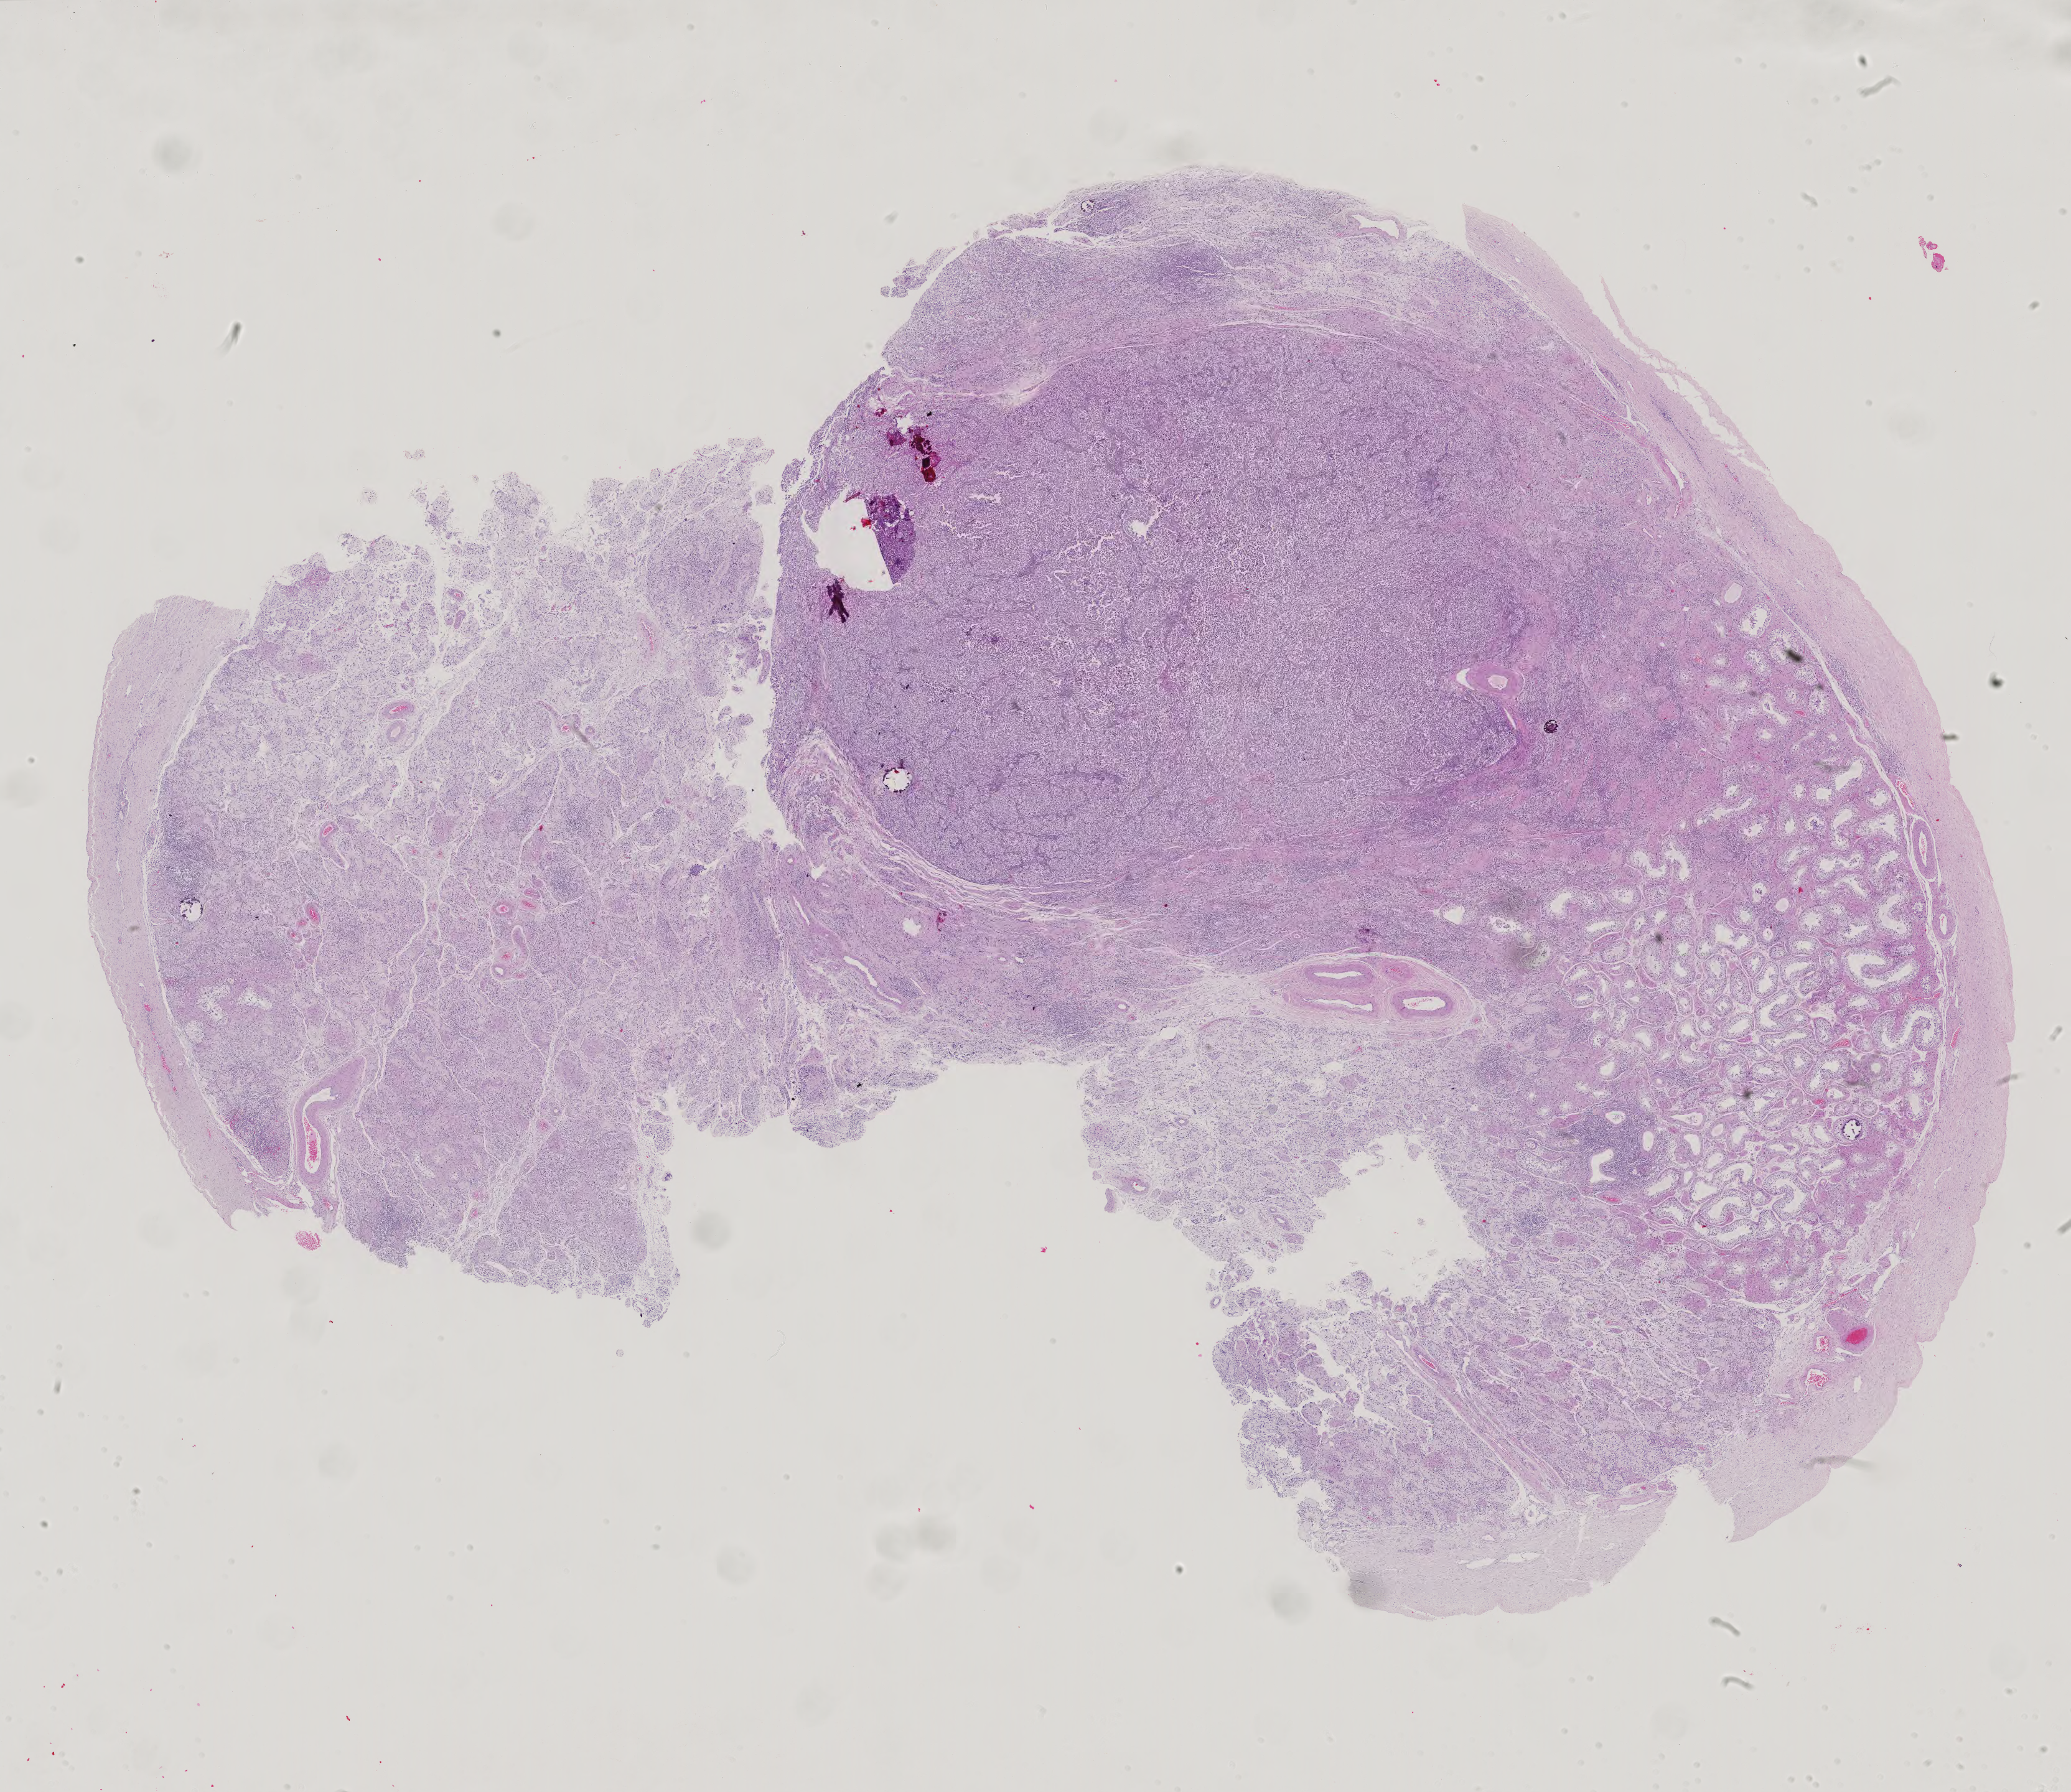
H&E-stained whole-slide image, low-resolution overview of the scanned area, about 24.2 x 21.0 mm (acquisition: 40x scan), formalin-fixed paraffin-embedded (FFPE) diagnostic section, additional new primary tumour sample from the testis. Male patient; age at initial diagnosis 31 years.
This section: additional new primary tumour. Patient diagnosis: Seminoma, NOS.